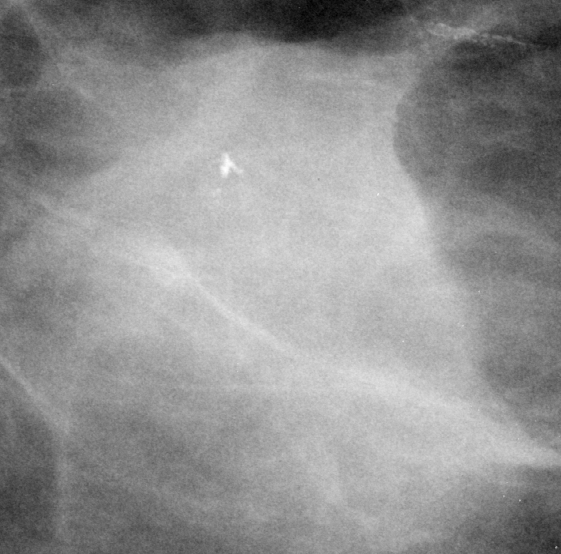
Crop from a digitized film mammogram around one marked abnormality, left breast, CC view.
Marked abnormality: mass, shape irregular, margins ill defined; BI-RADS assessment category 4; pathology (as recorded): malignant.